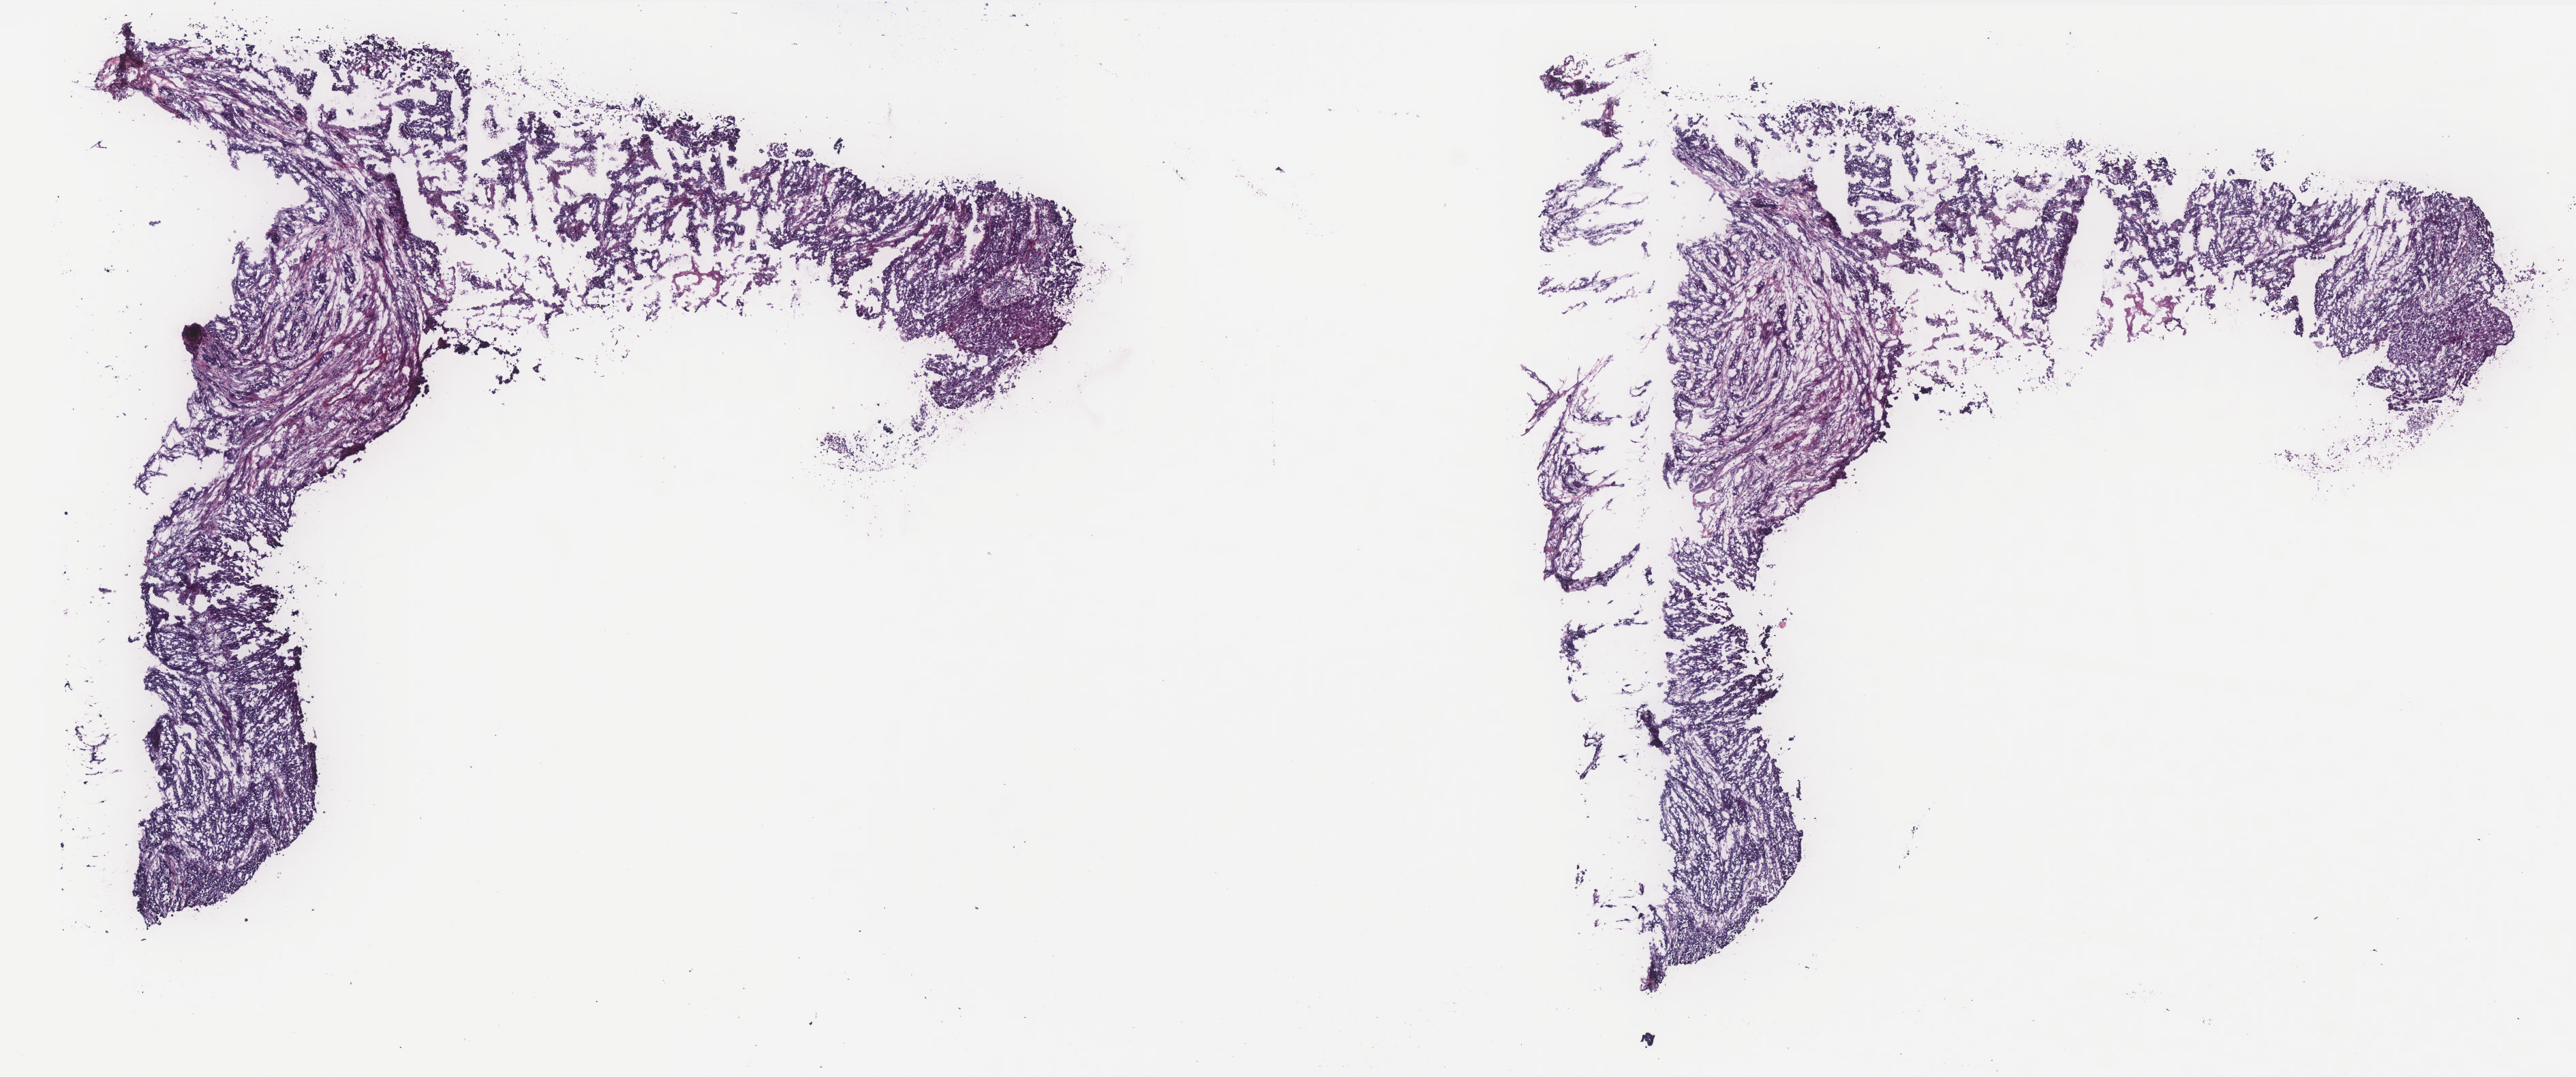
Whole-slide histology image, H&E-stained — whole scanned area (about 15.2 x 6.3 mm) shown as a low-resolution overview. Frozen section. Cervix, primary tumour sample. Female, age 51 years at initial diagnosis. Histologic grade: G3 (poorly differentiated). Slide review estimates, as recorded: tumour cells 80%, tumour nuclei 75%, normal cells 0%, stromal cells 20%, necrosis 0%. Inflammatory infiltration, as recorded: lymphocyte infiltration 0%, monocyte infiltration 0%, neutrophil infiltration 0%.
Histologic diagnosis: Squamous cell carcinoma, NOS (cervix uteri).